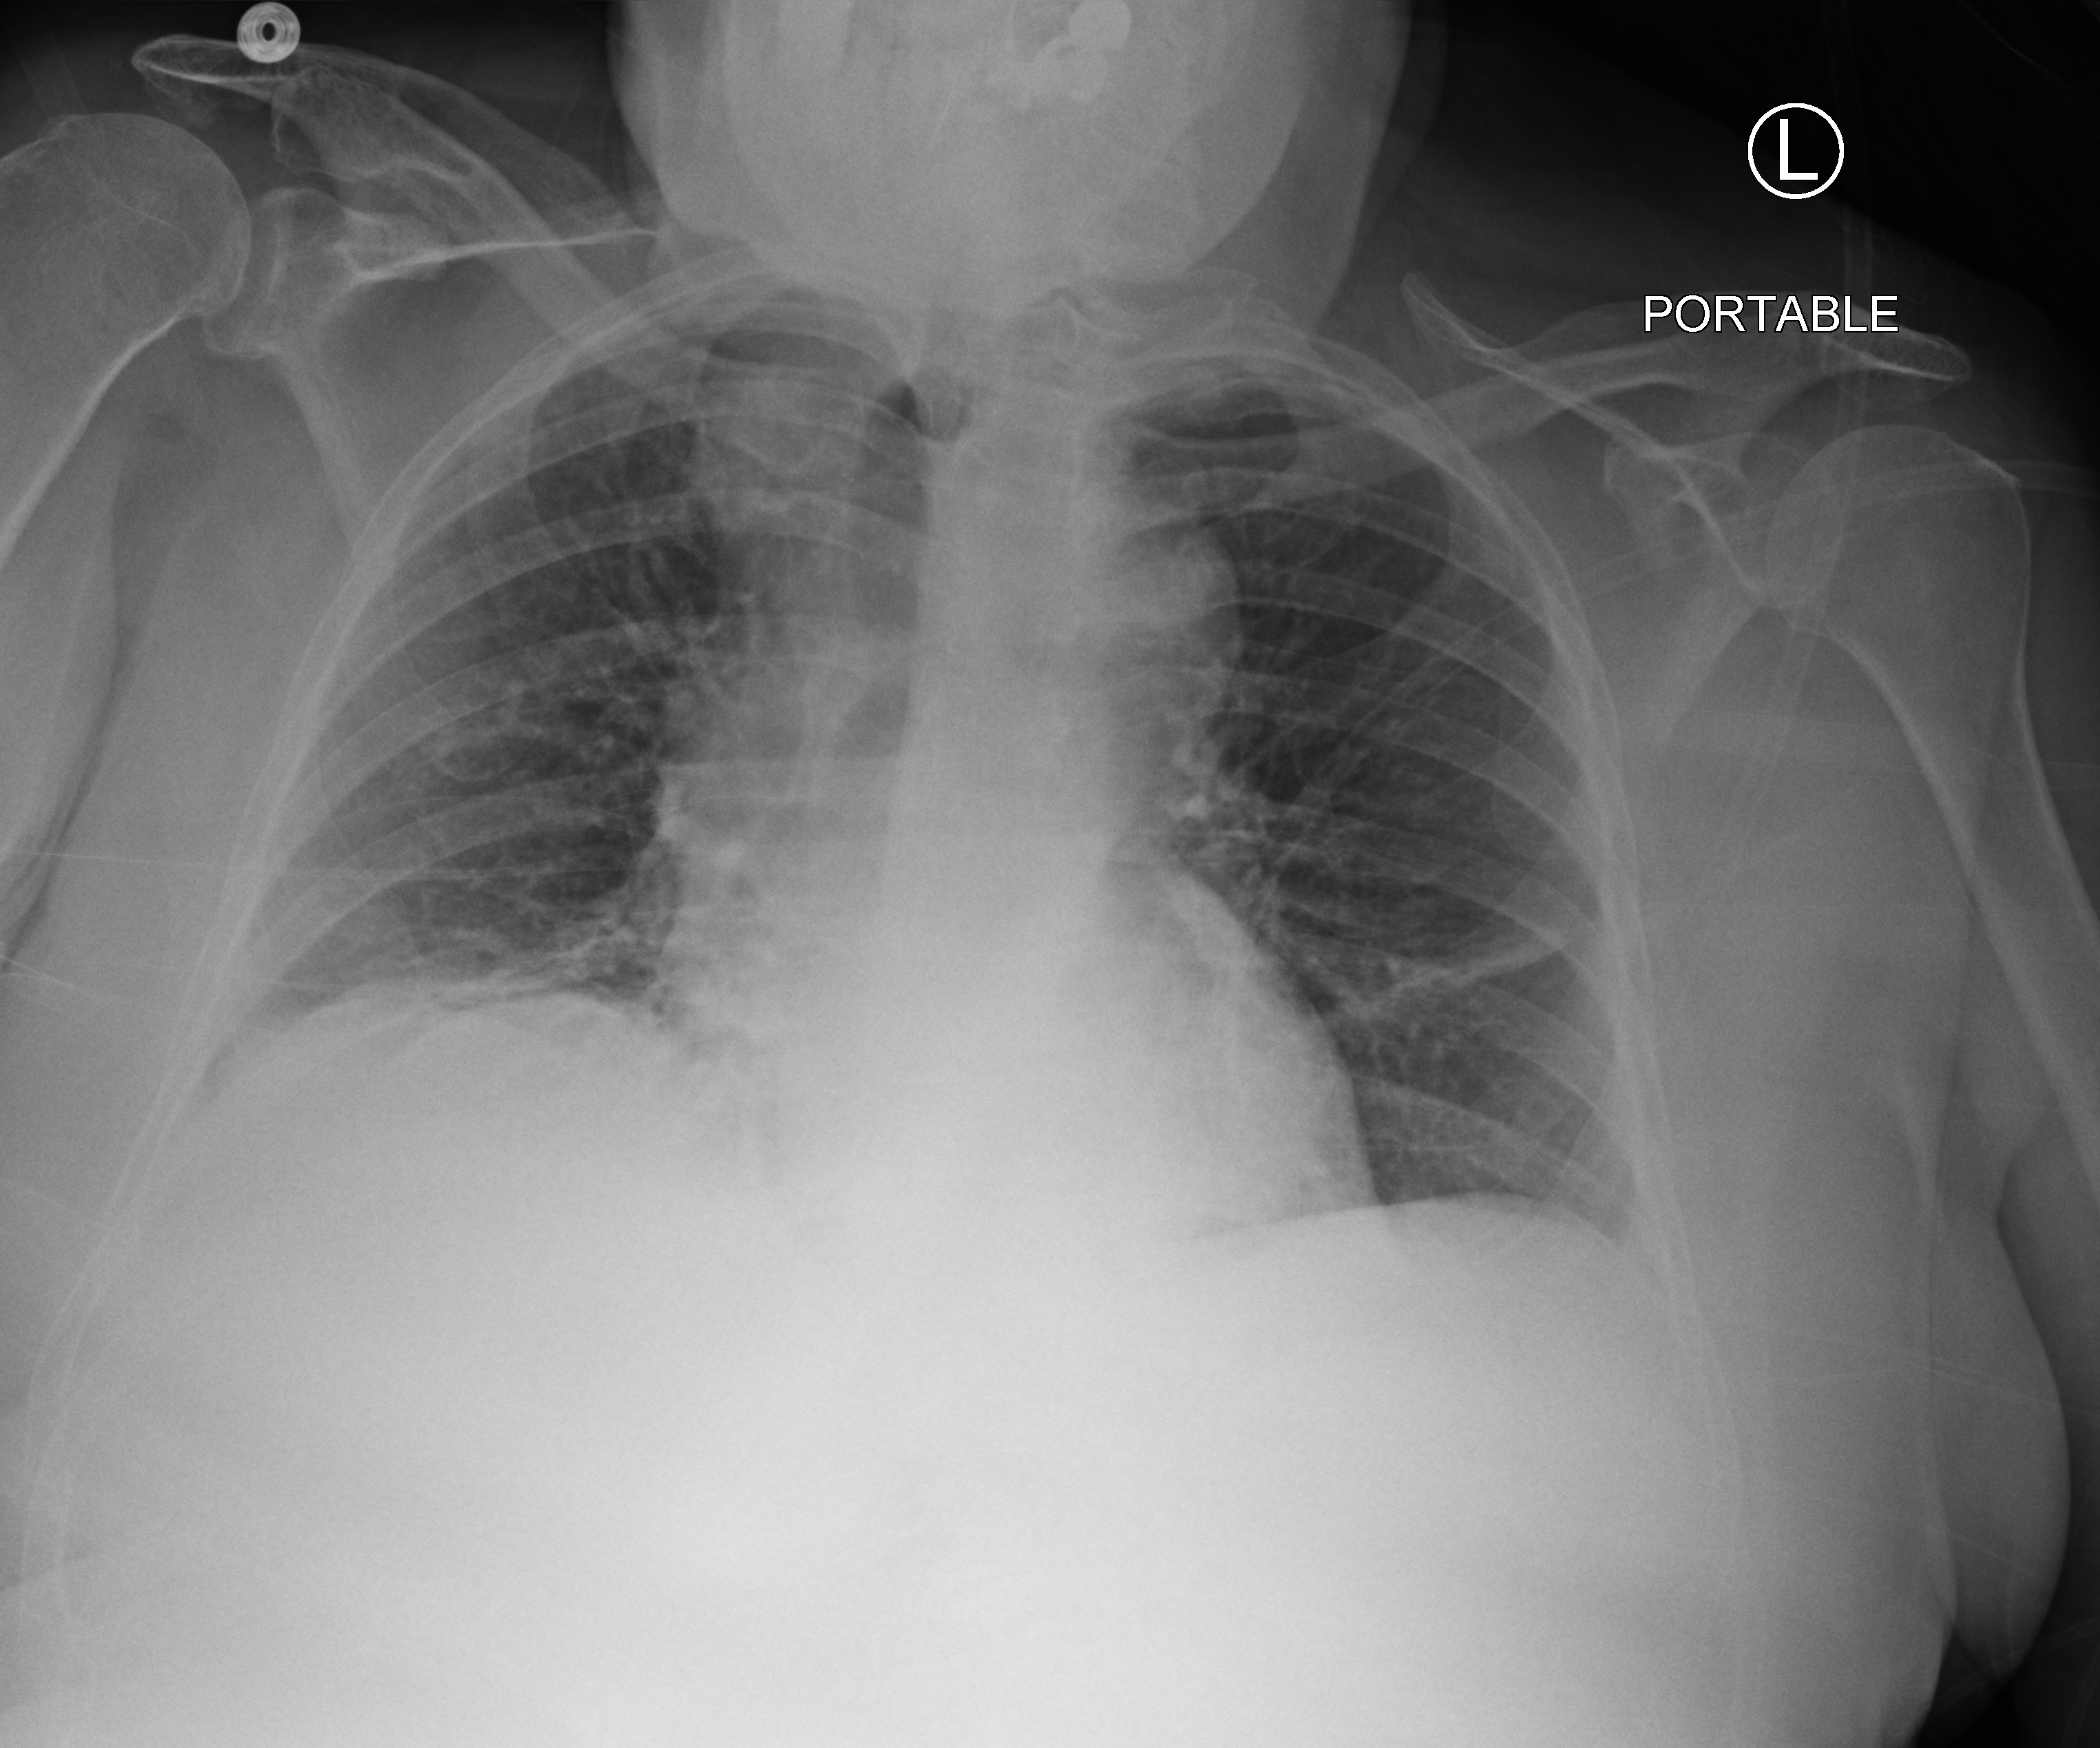
Chest X-ray (portable), anteroposterior (AP) projection. Female patient hospitalised with COVID-19, age 75–90 years.
Hospital-stay facts (about this admission, not read from this image; timing relative to this image not recorded): mechanically ventilated during this hospital stay: no; admitted to intensive care during this hospital stay: no; length of hospital stay: 14 days.